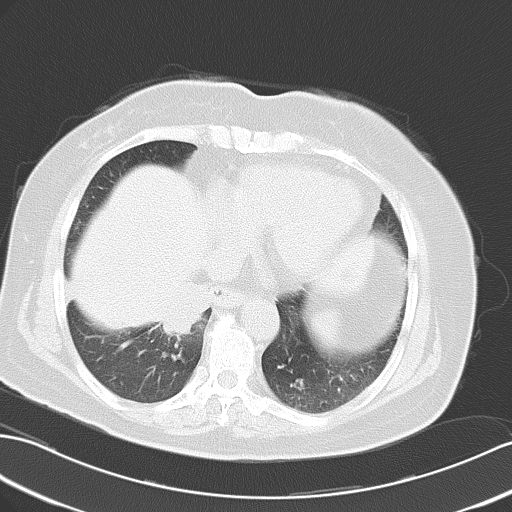
Chest CT, one axial slice; slice 17 of 50 in the series (ordered by position); reconstruction kernel B70f; 120 kVp; lung window (W 1500 / L -600 HU); 5 mm slice thickness; 512 × 512 image matrix, field of view 353 × 353 mm. Patient: female, 63 years. From the clinical record (not read from this slice): clinical TNM (as recorded): T3 N0 M0.
Structures marked on this image (bounding box drawn by a radiologist):
- lung tumour (recorded histology: adenocarcinoma): bounding box (x1, y1, x2, y2) in pixels: (157, 280, 213, 340)